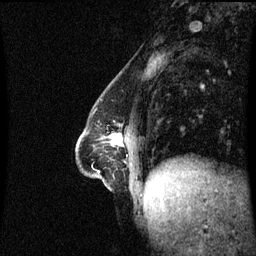
Breast MRI (dynamic contrast-enhanced), one sagittal slice. Slice 24 of 60 in the series (ordered by position). Dynamic contrast-enhanced series, image 2 of 3 at this slice position (ordered by acquisition). 1.5 T. TE 4.2 ms, TR 8.9 ms. 2.2 mm slice thickness. 256 × 256 image matrix, field of view 210 × 210 mm. Patient: female, 47 years. Case-level facts recorded for this patient, not image findings: setting: breast cancer imaged before/during neoadjuvant chemotherapy; receptor status: HR-positive, HER2-negative.
Annotated regions visible in this slice (semi-automatic segmentation, software-assisted and operator-edited):
- analysis volume of interest (the breast-tissue region the enhancement analysis was run in; not a lesion): box from (x=77, y=128) to (x=141, y=188) px
- tumour enhancement mask (voxels above the 70 % enhancement threshold inside the analysis volume of interest): (x=112, y=136)–(x=122, y=144)